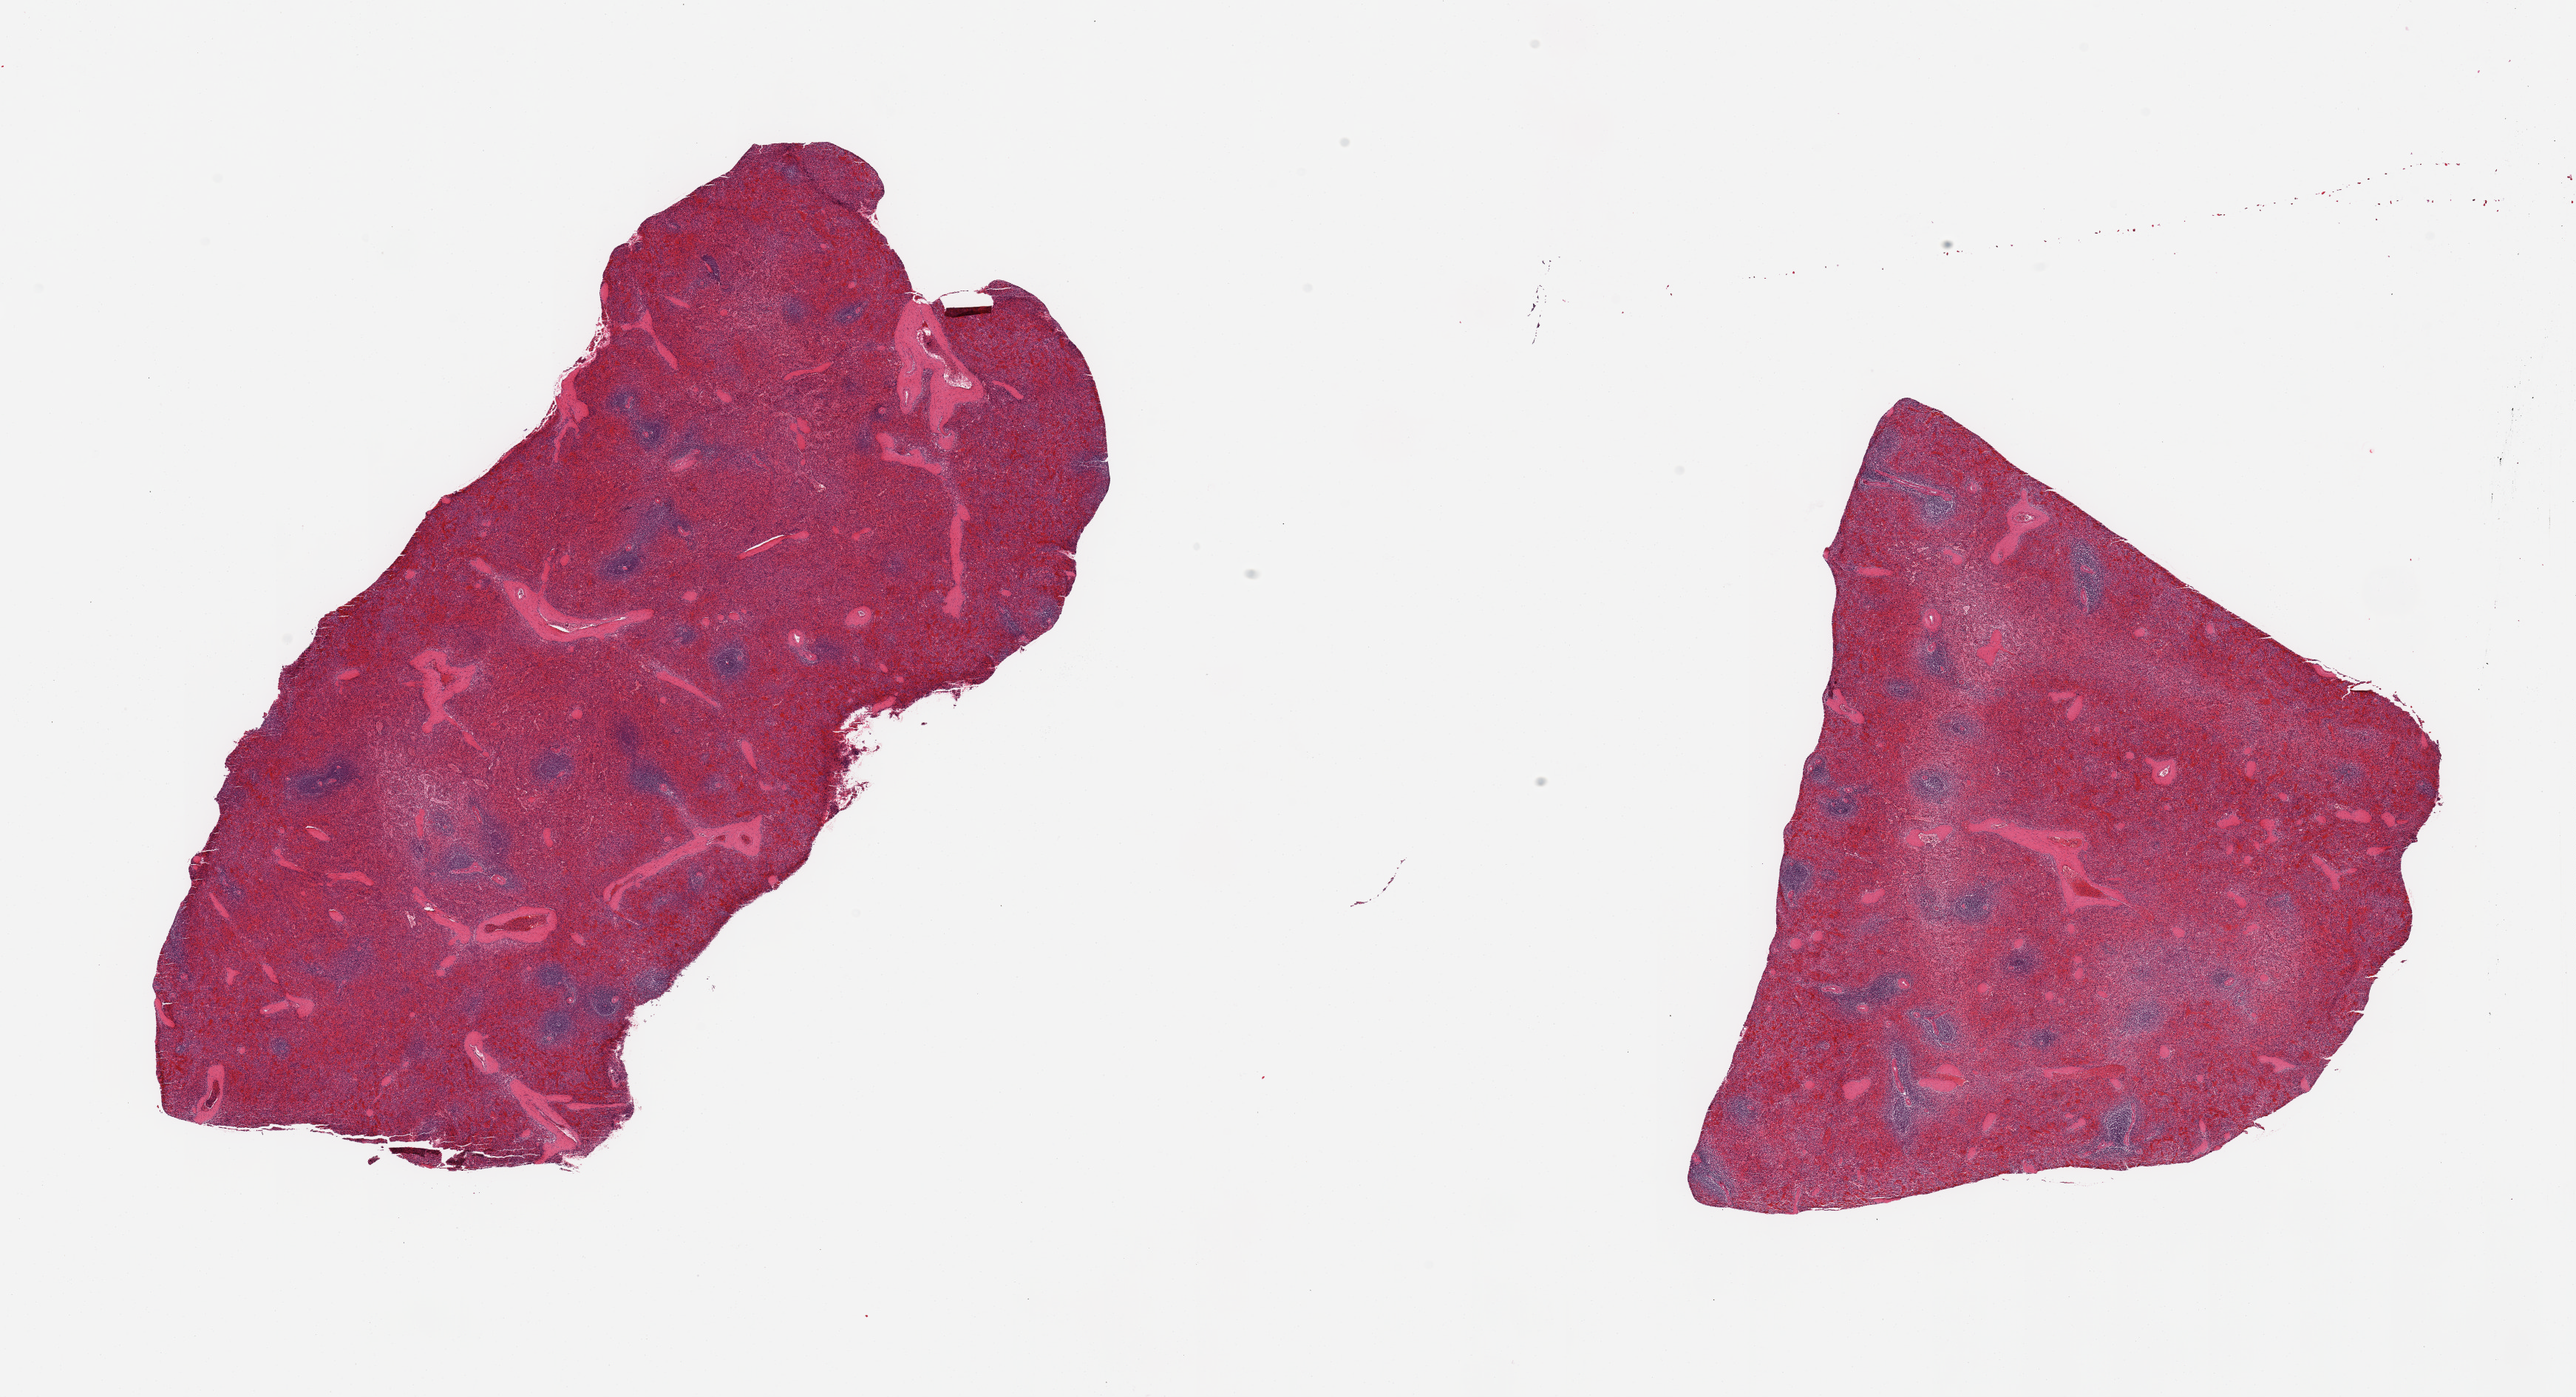
Whole-slide image, haematoxylin and eosin stain — whole scanned area (about 27.6 x 14.9 mm, slide scanned at 20x) shown as a low-resolution overview. PAXgene-fixed, paraffin-embedded tissue. Section of spleen (target tissue). Tissue donor sample. Donor: male.
Reviewer comment on this tissue sample: 2 pieces; congested.